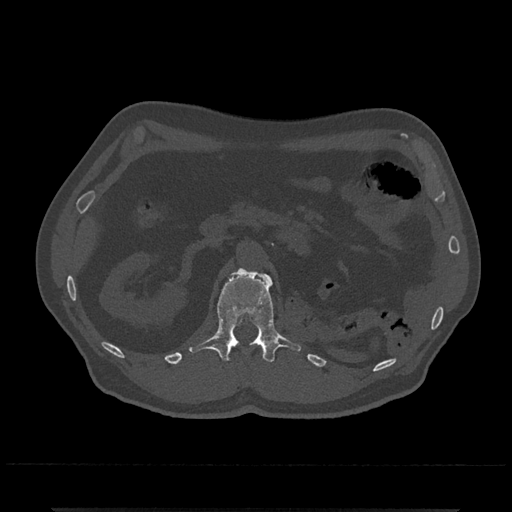
CT including the spine, one axial slice; slice 368 of 797 in the series (ordered by position); reconstruction kernel Br40s/3; bone window (W 1800 / L 400 HU); 512 × 512 image matrix, field of view 393 × 393 mm. Male patient, age 67 years. Case-level facts recorded for this patient, not image findings: primary cancer: prostate.
Outlined on this slice (semi-automatic segmentation, software-assisted and operator-edited):
- L1 vertebra: bounding box [x1, y1, x2, y2] px = [188, 268, 302, 362]
- T12 vertebra: [256, 343, 263, 349]